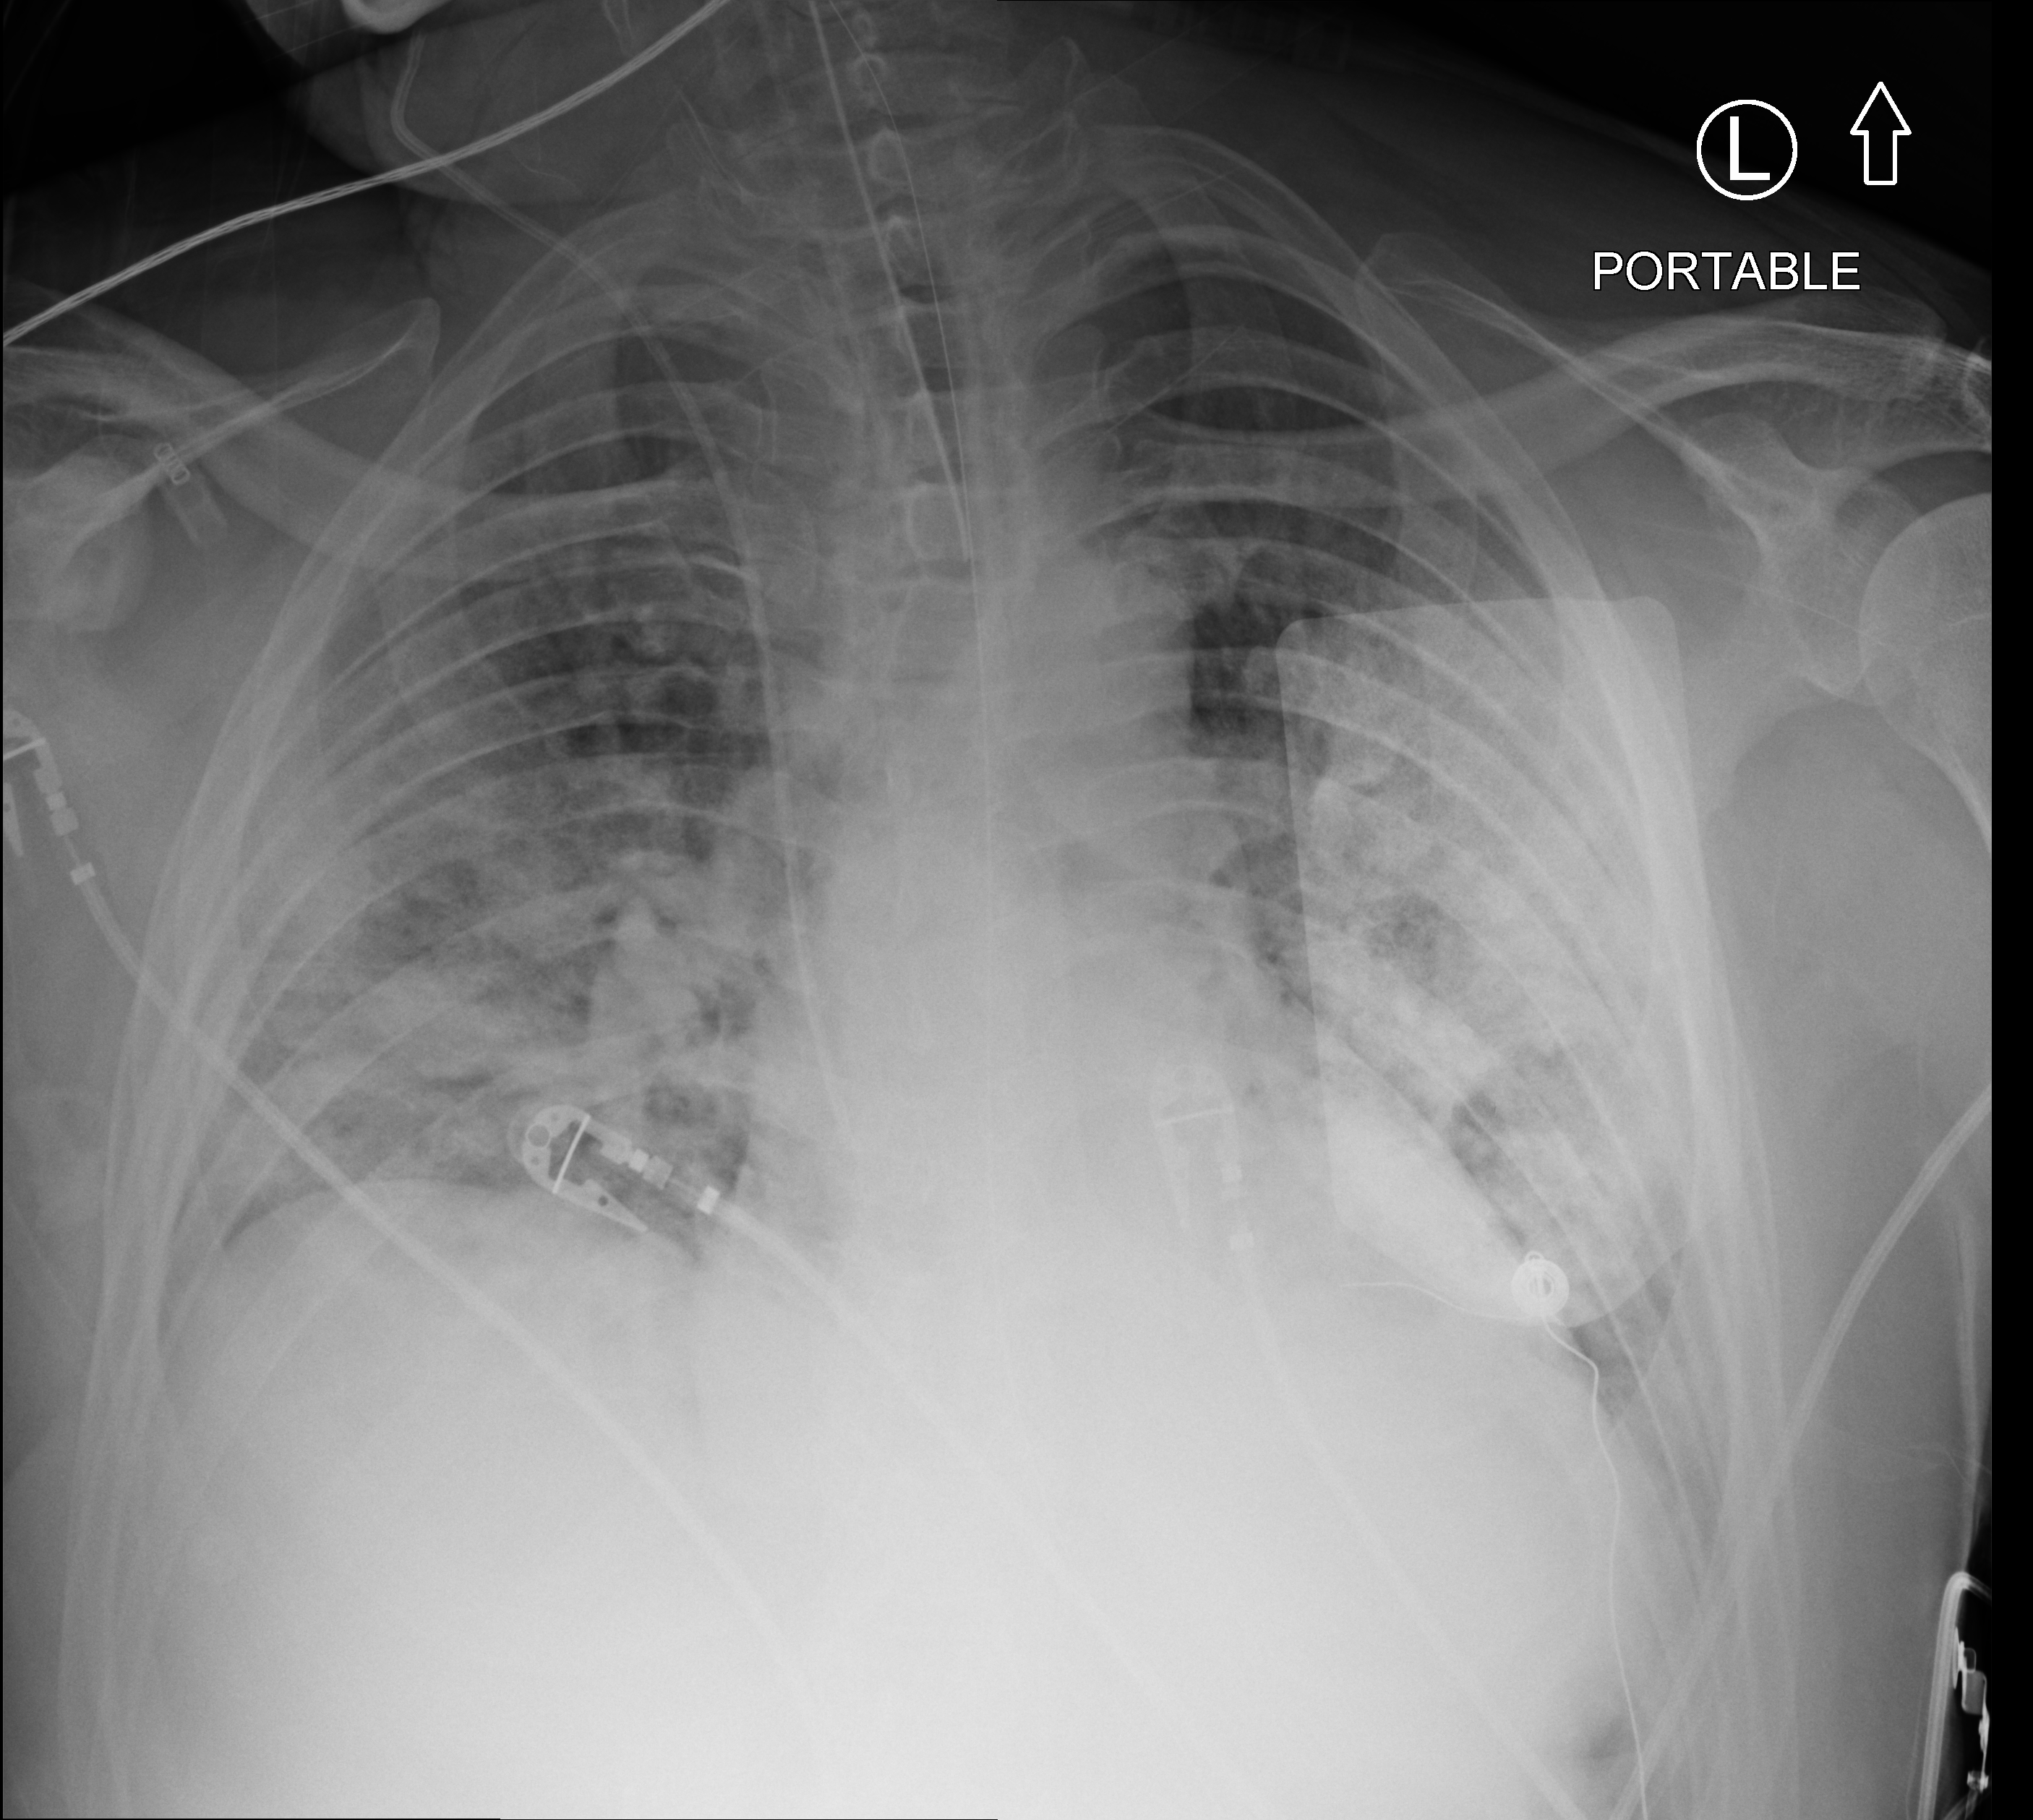
Bedside chest radiograph (computed radiography), anteroposterior (AP) projection. Male patient hospitalised with COVID-19, age 18–59 years.
Admission-level facts for this patient (not findings on this image; timing relative to this image not recorded): admitted to intensive care during this hospital stay: yes; mechanically ventilated during this hospital stay: yes.